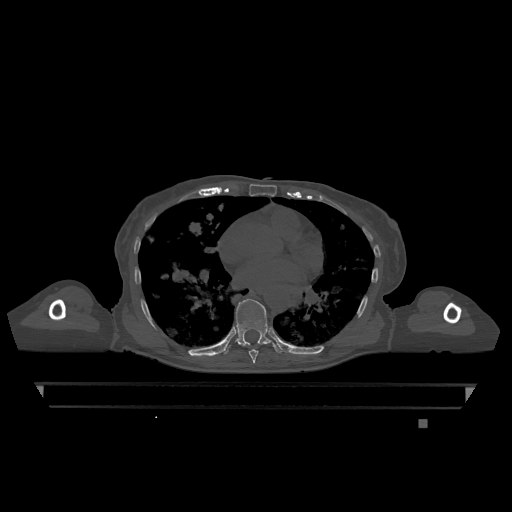
CT including the spine, one axial slice; position 709 of 1317 along the scan axis; bone window (W 1800 / L 400 HU); 0.5 mm slice thickness; 512 × 512 image matrix, field of view 500 × 500 mm. Patient: female, 74 years. From the clinical record (not read from this slice): primary cancer: lung; vertebrae with lytic lesions (as recorded): T1, T4, T5, T6, L4, L5.
Outlined on this slice (semi-automatic segmentation, software-assisted and operator-edited):
- T7 vertebra: bounding box (x1, y1, x2, y2) in pixels: (249, 349, 259, 363)
- T9 vertebra: (223, 299, 283, 354)